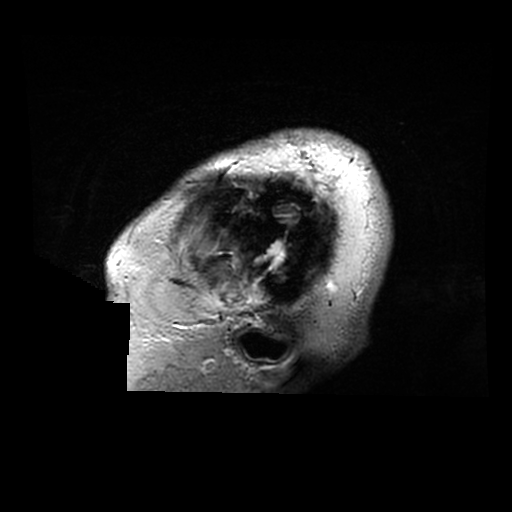
Brain MRI from a brain-tumour surgery series, one sagittal slice. Slice 266 of 320 in the series (ordered by position). 0.6 mm slice thickness. 512 × 512 image matrix, field of view 240 × 240 mm. From the clinical record (not read from this slice): histopathology: Astrocytoma; WHO grade: 2; IDH mutation: yes.
Structures marked on this image (outlined manually by an expert reader):
- tumour: bounding box [x1, y1, x2, y2] px = [257, 241, 287, 269]